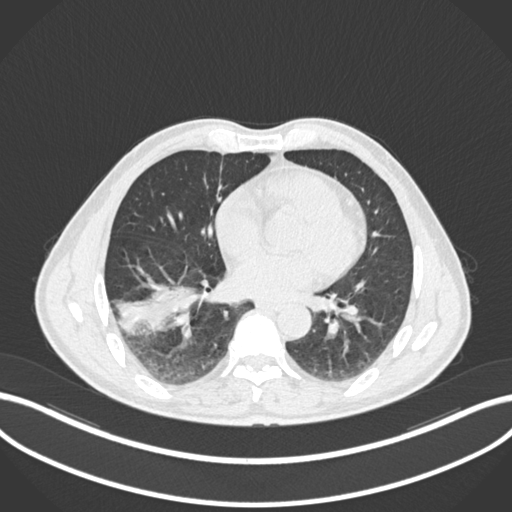
Chest CT, one axial slice; position 78 of 208 along the scan axis; 120 kVp; lung window (W 1500 / L -600 HU); 1 mm slice thickness; 512 × 512 image matrix, field of view 400 × 400 mm. Patient: male, 58 years. Case-level facts recorded for this patient, not image findings: clinical TNM (as recorded): T3 N0 M0.
Structures marked on this image (rectangle marked by the reading radiologist):
- lung tumour (recorded histology: squamous cell carcinoma): bounding box [x1, y1, x2, y2] px = [112, 271, 200, 339]